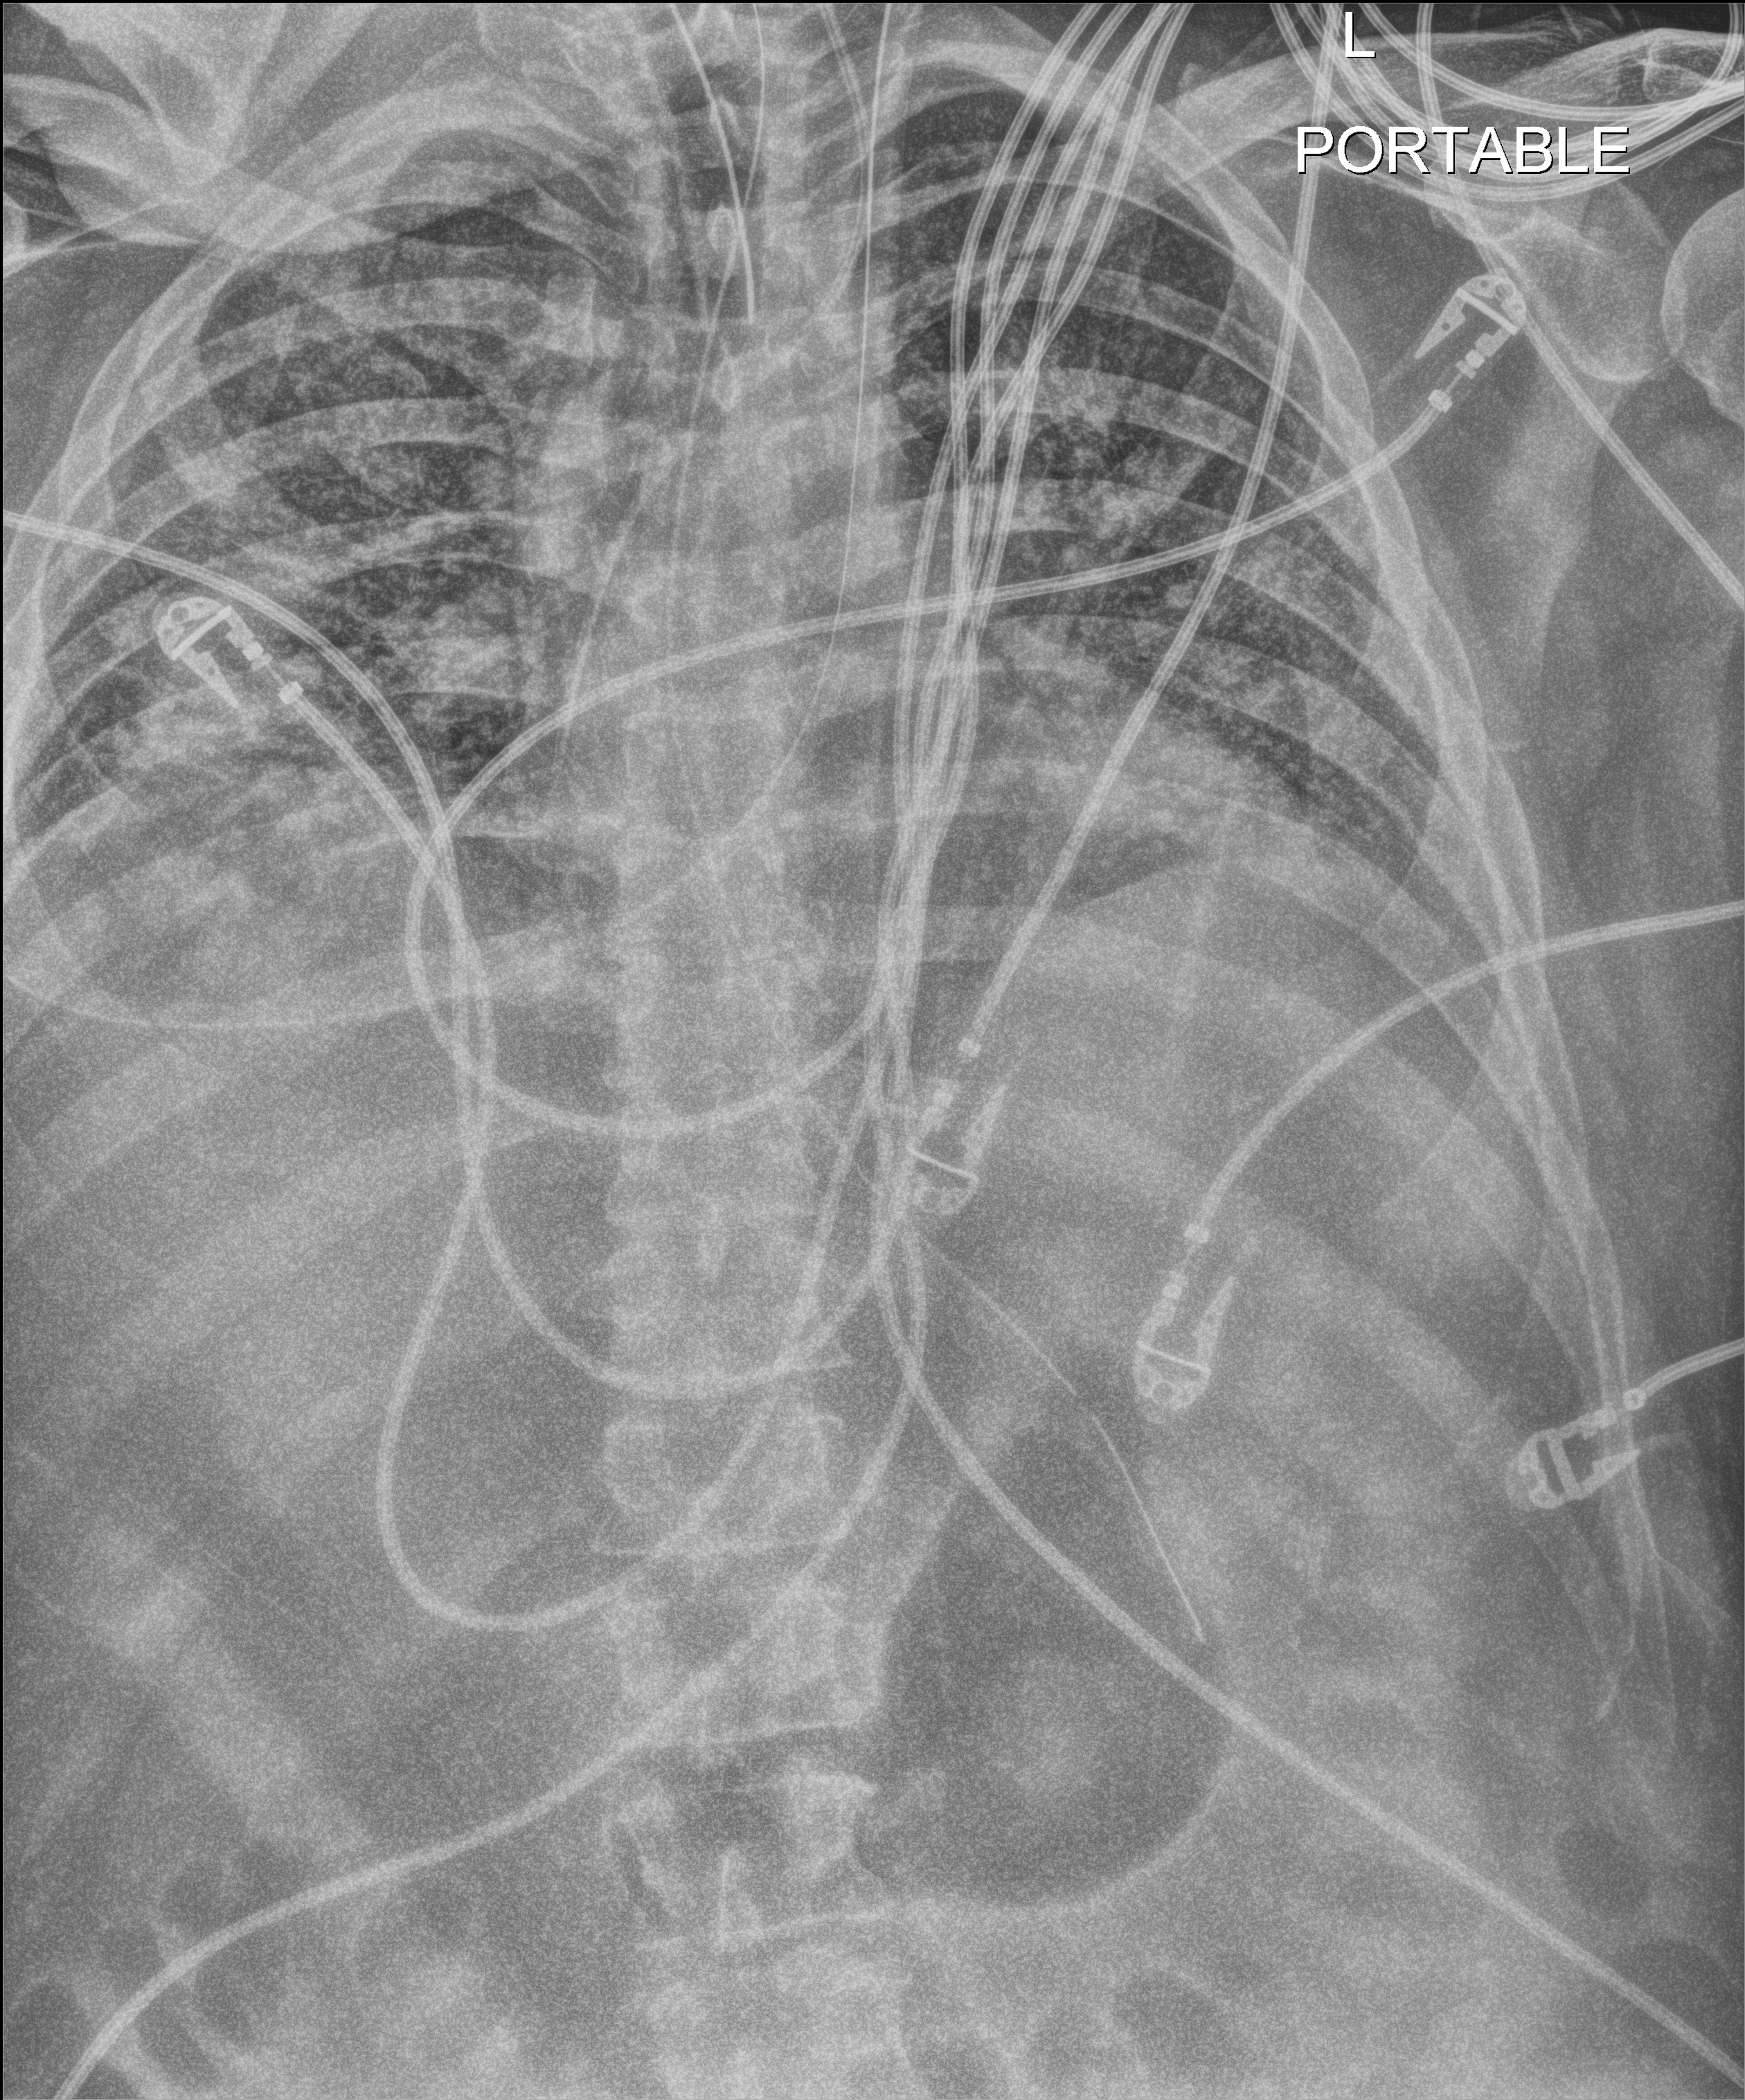
Chest X-ray (portable); anteroposterior (AP) projection. Patient hospitalised with COVID-19; male, aged 18–59 years.
From the hospital-stay record, not from the radiograph (when in the stay this image was taken is not recorded):
- length of hospital stay: 80 days
- admitted to intensive care during this hospital stay: yes